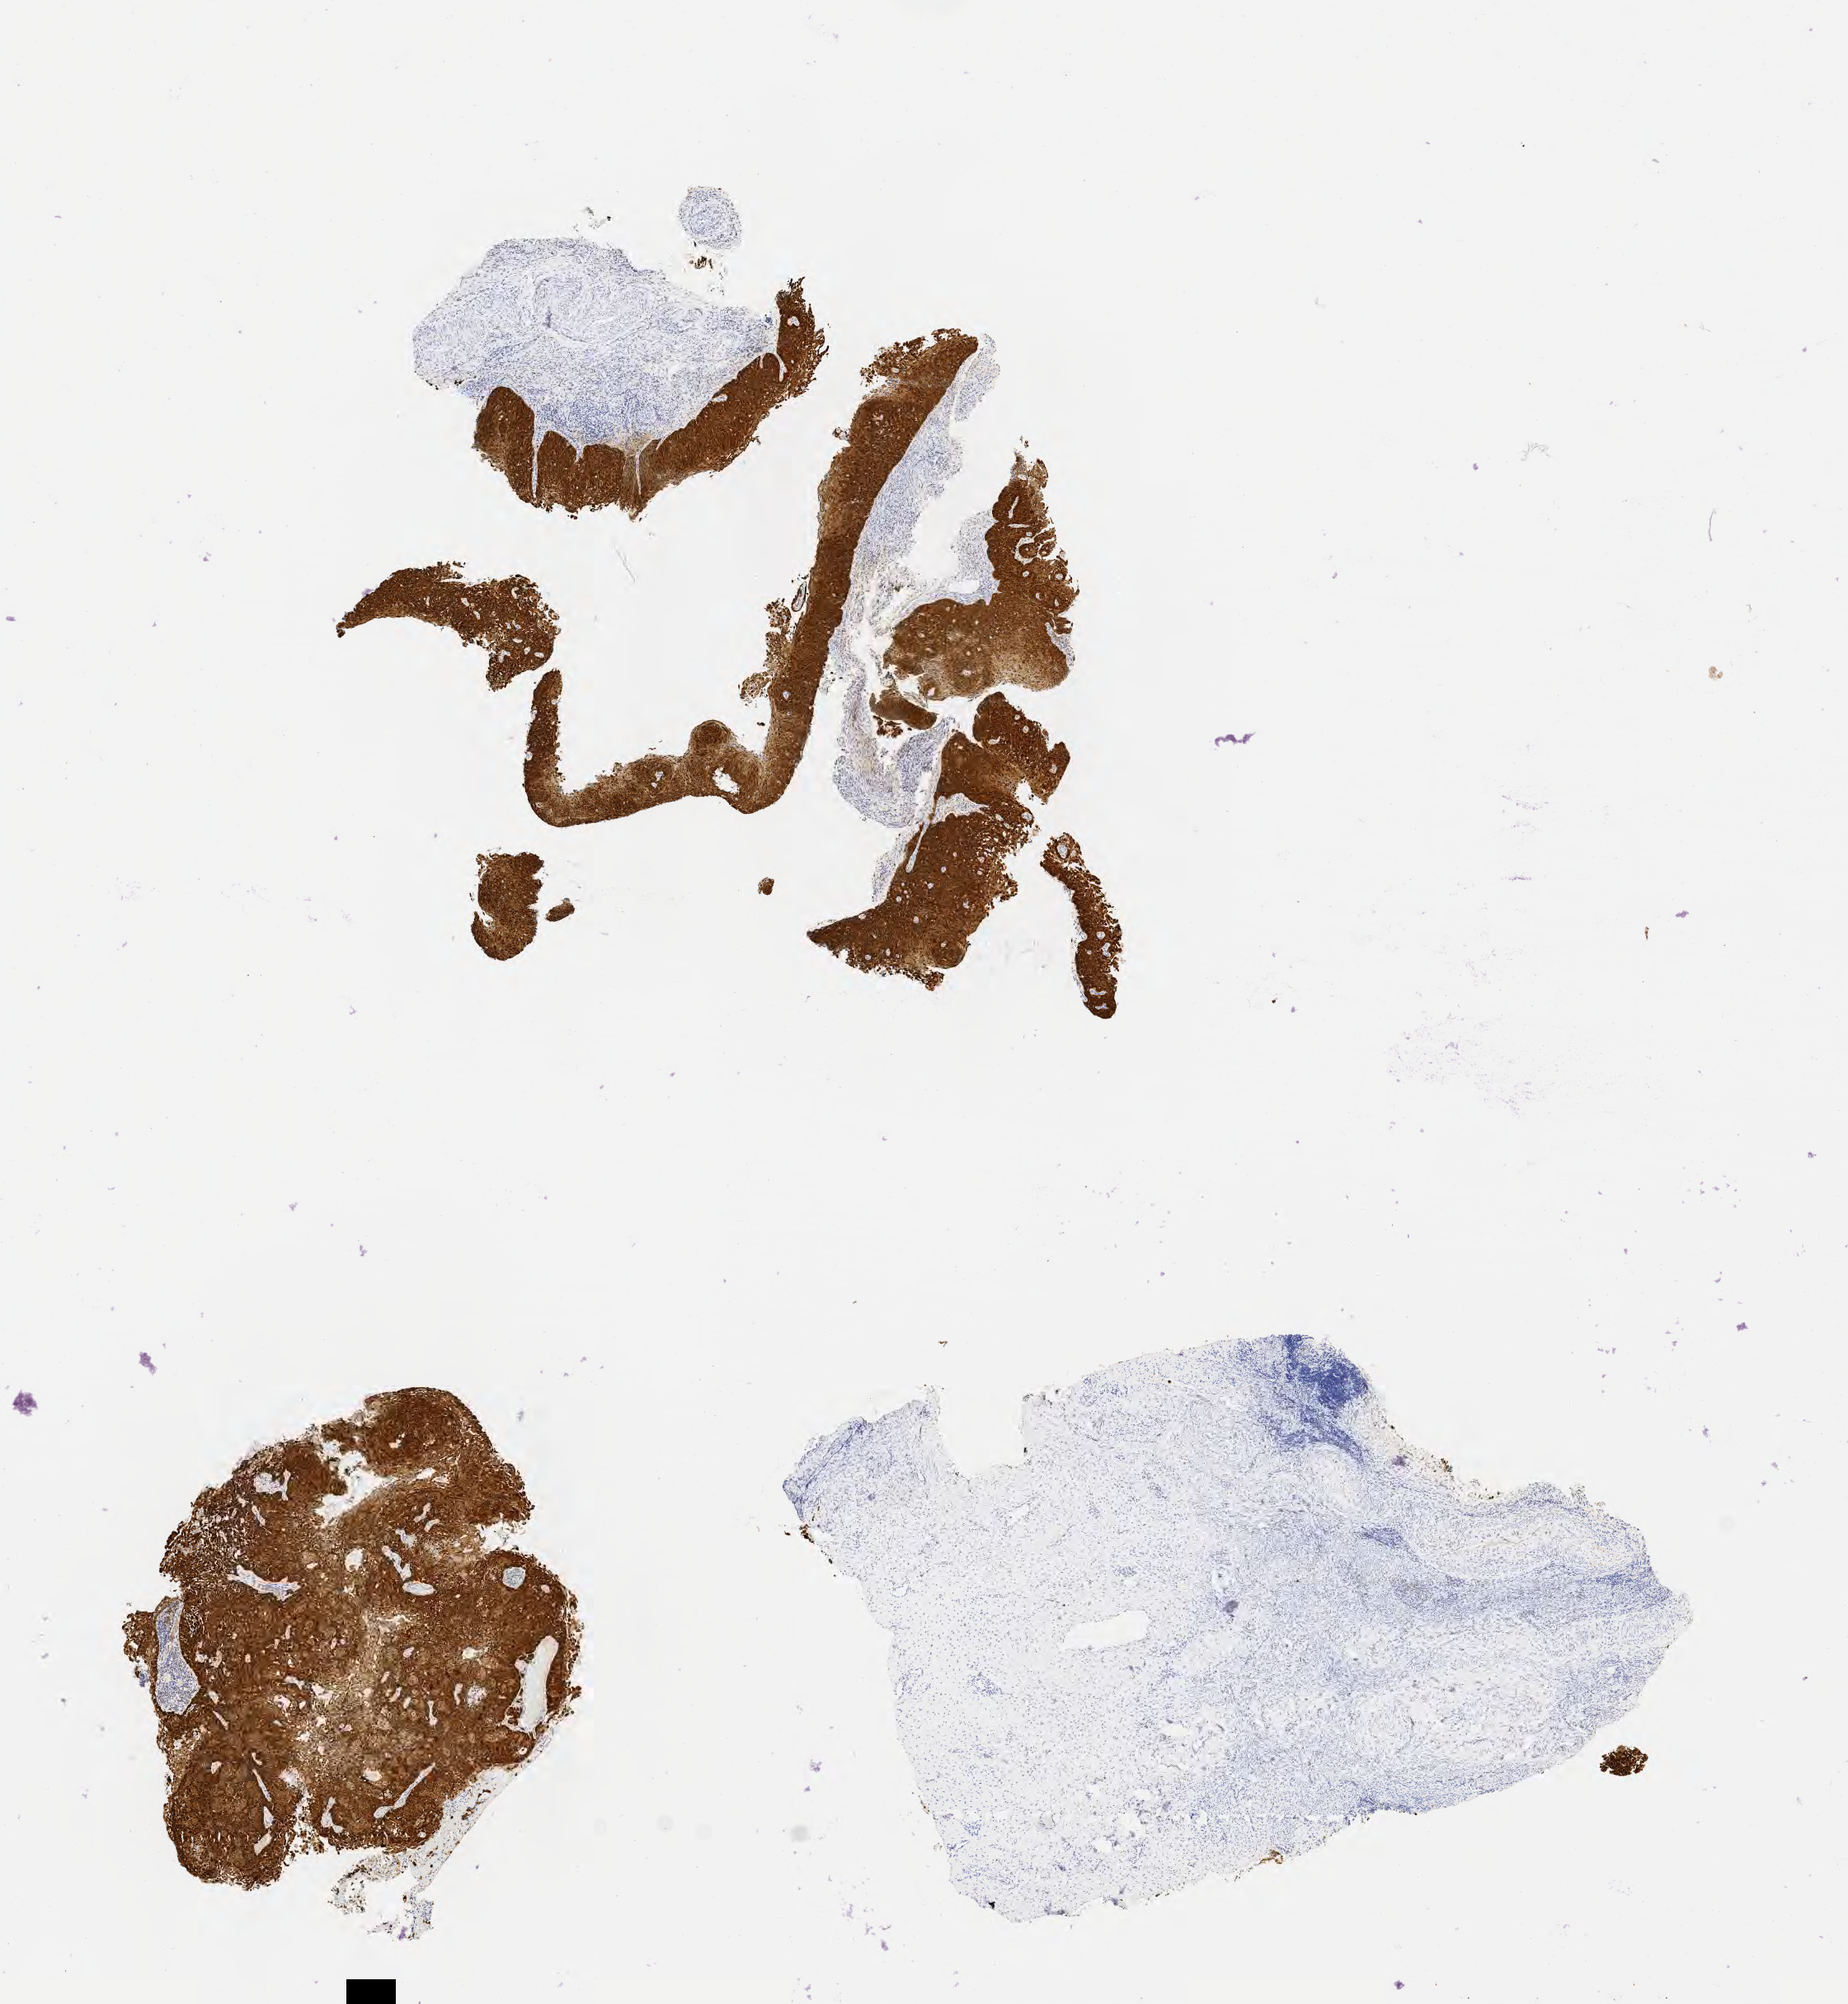
Whole-slide image, immunohistochemical stain for p16 (p16INK4a) — low-resolution overview of the scanned area, about 9.1 x 9.8 mm. Specimen: tumor tissue. Anatomic site: cervix. Female patient, aged 60.
Histologic diagnosis: Squamous cell carcinoma, large cell, nonkeratinizing, NOS.